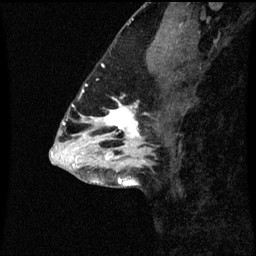
Breast MRI (dynamic contrast-enhanced), one sagittal slice. Slice 29 of 60 in the series (ordered by position). Dynamic contrast-enhanced series, image 2 of 3 at this slice position (ordered by acquisition). 1.5 T. TE 4.2 ms, TR 8.9 ms. 256 × 256 image matrix, field of view 200 × 200 mm. Patient: female, 43 years. Case-level facts recorded for this patient, not image findings: setting: breast cancer imaged before/during neoadjuvant chemotherapy; receptor status: HR-positive, HER2-negative.
Outlined on this slice (semi-automatically segmented with operator editing):
- analysis volume of interest (the breast-tissue region the enhancement analysis was run in; not a lesion): box from (x=96, y=100) to (x=155, y=159) px
- tumour enhancement mask (voxels above the 70 % enhancement threshold inside the analysis volume of interest): (x=106, y=100)–(x=141, y=157)